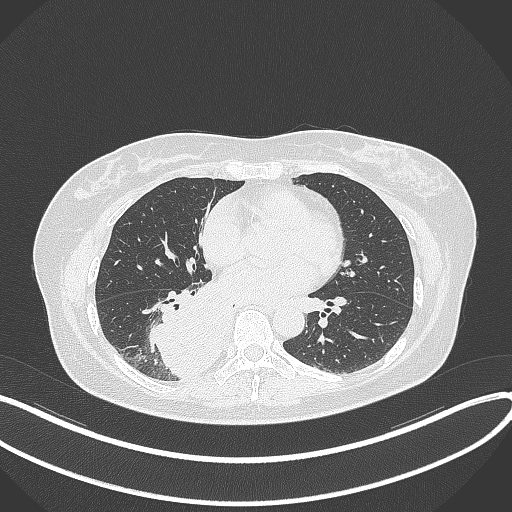
Chest CT, one axial slice; position 160 of 331 along the scan axis; lung window (W 1500 / L -600 HU); 1 mm slice thickness; 512 × 512 image matrix, field of view 400 × 400 mm. Female patient, age 54 years. Case-level facts recorded for this patient, not image findings: clinical TNM (as recorded): T4 N0 M0.
Annotated regions visible in this slice (bounding box drawn by a radiologist):
- lung tumour (recorded histology: adenocarcinoma): bounding box (x1, y1, x2, y2) in pixels: (140, 283, 227, 381)